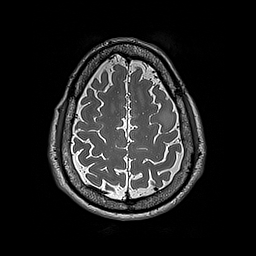
Brain MRI from a brain-tumour surgery series, one axial slice; slice 60 of 192 in the series (ordered by position); 1 mm slice thickness; 256 × 256 image matrix, field of view 250 × 250 mm. Case-level facts recorded for this patient, not image findings: histopathology: Astrocytoma; WHO grade: 2; IDH mutation: yes; tumour location: Left Frontal.
Outlined on this slice (expert manual segmentation):
- tumour: bounding box [x1, y1, x2, y2] px = [158, 105, 173, 128]